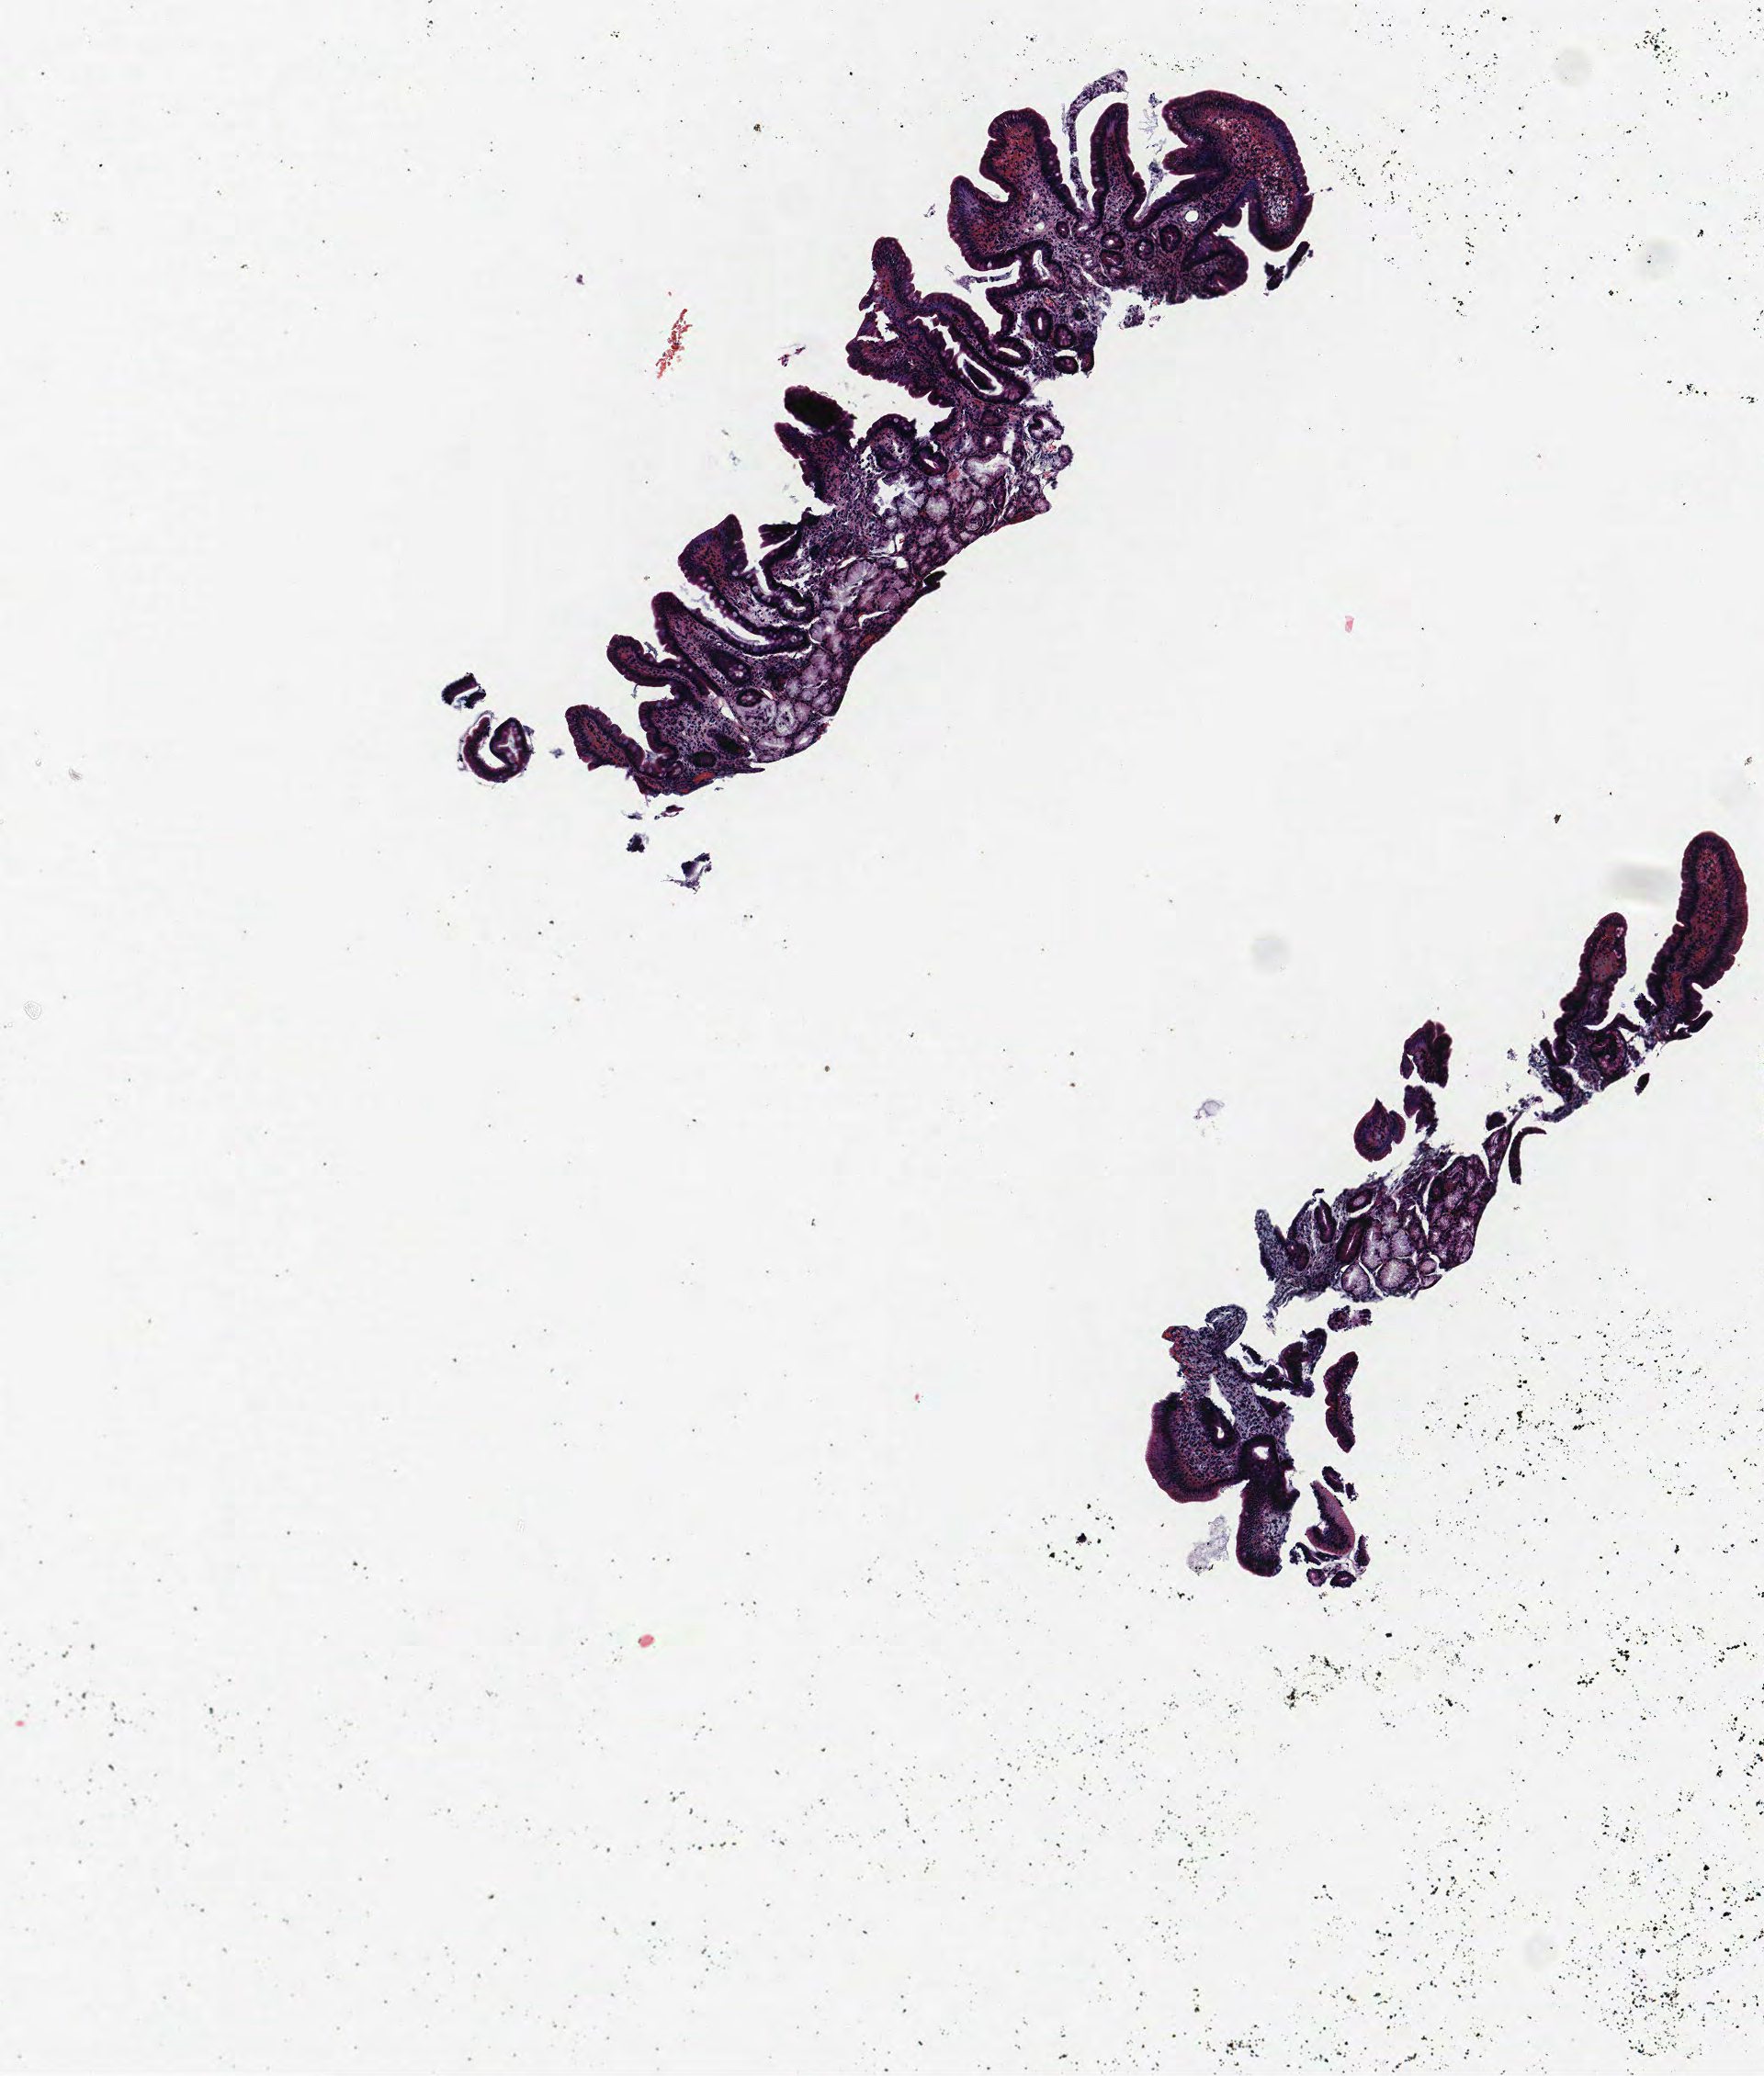
Whole-slide histology image, Hematoxylin and eosin (H&E) stained, shown as a low-resolution overview of the whole scanned area (about 3.8 x 4.5 mm); formalin-fixed paraffin-embedded (FFPE) section; lung. Male patient, aged 57 at enrolment.
Participant's lung-cancer diagnosis: Squamous cell carcinoma, NOS.